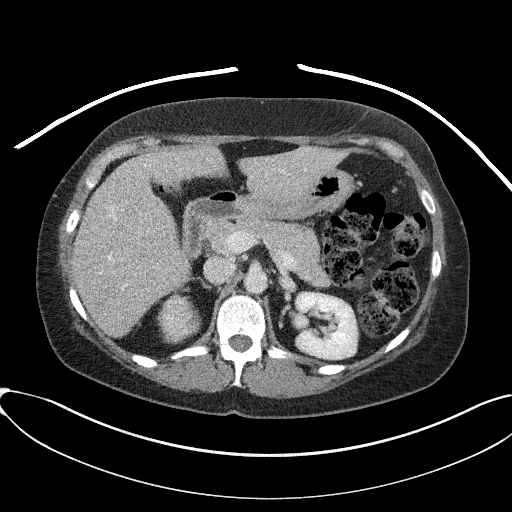
Contrast-enhanced abdominal CT, one axial slice. Slice 49 of 95 in the series (ordered by position). Reconstruction kernel I41f/2. 100 kVp. Soft-tissue window (W 400 / L 40 HU). 512 × 512 image matrix, field of view 410 × 410 mm. Patient: female, 46 years. From the clinical record (not read from this slice): diagnosis: adrenocortical carcinoma; tumour side: right adrenal; tumour size at pathology: 7.2 cm; Ki-67 index: 50 %; stage (as recorded): 4.
Structures marked on this image (semi-automatically segmented with operator editing):
- mass: bounding box (x1, y1, x2, y2) in pixels: (161, 296, 197, 341)